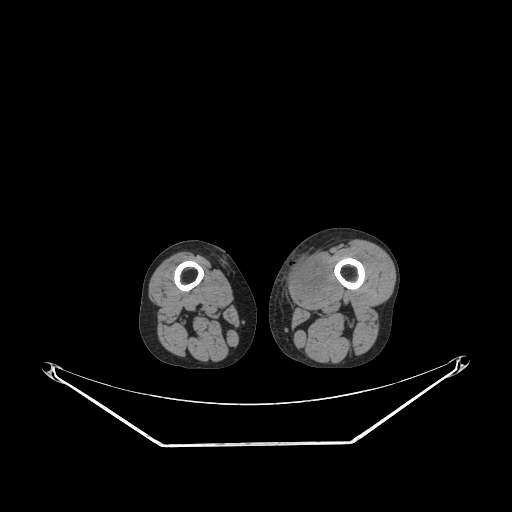
CT of an extremity soft-tissue mass (from a PET/CT study), one axial slice. Position 210 of 267 along the scan axis. Reconstruction kernel STANDARD. Soft-tissue window (W 400 / L 40 HU). 3.75 mm slice thickness. 512 × 512 image matrix, field of view 500 × 500 mm. Male patient. From the clinical record (not read from this slice): histological type: pleiomorphic leiomyosarcoma; grade: high; site of the primary tumour: left thigh.
Annotated regions visible in this slice (expert contour drawn on MRI and transferred to this co-registered scan by the dataset authors):
- gross tumour volume including surrounding oedema: bounding box <288,253,328,303> (left, top, right, bottom; pixels)
- gross tumour volume (mass): <288,256,325,291>